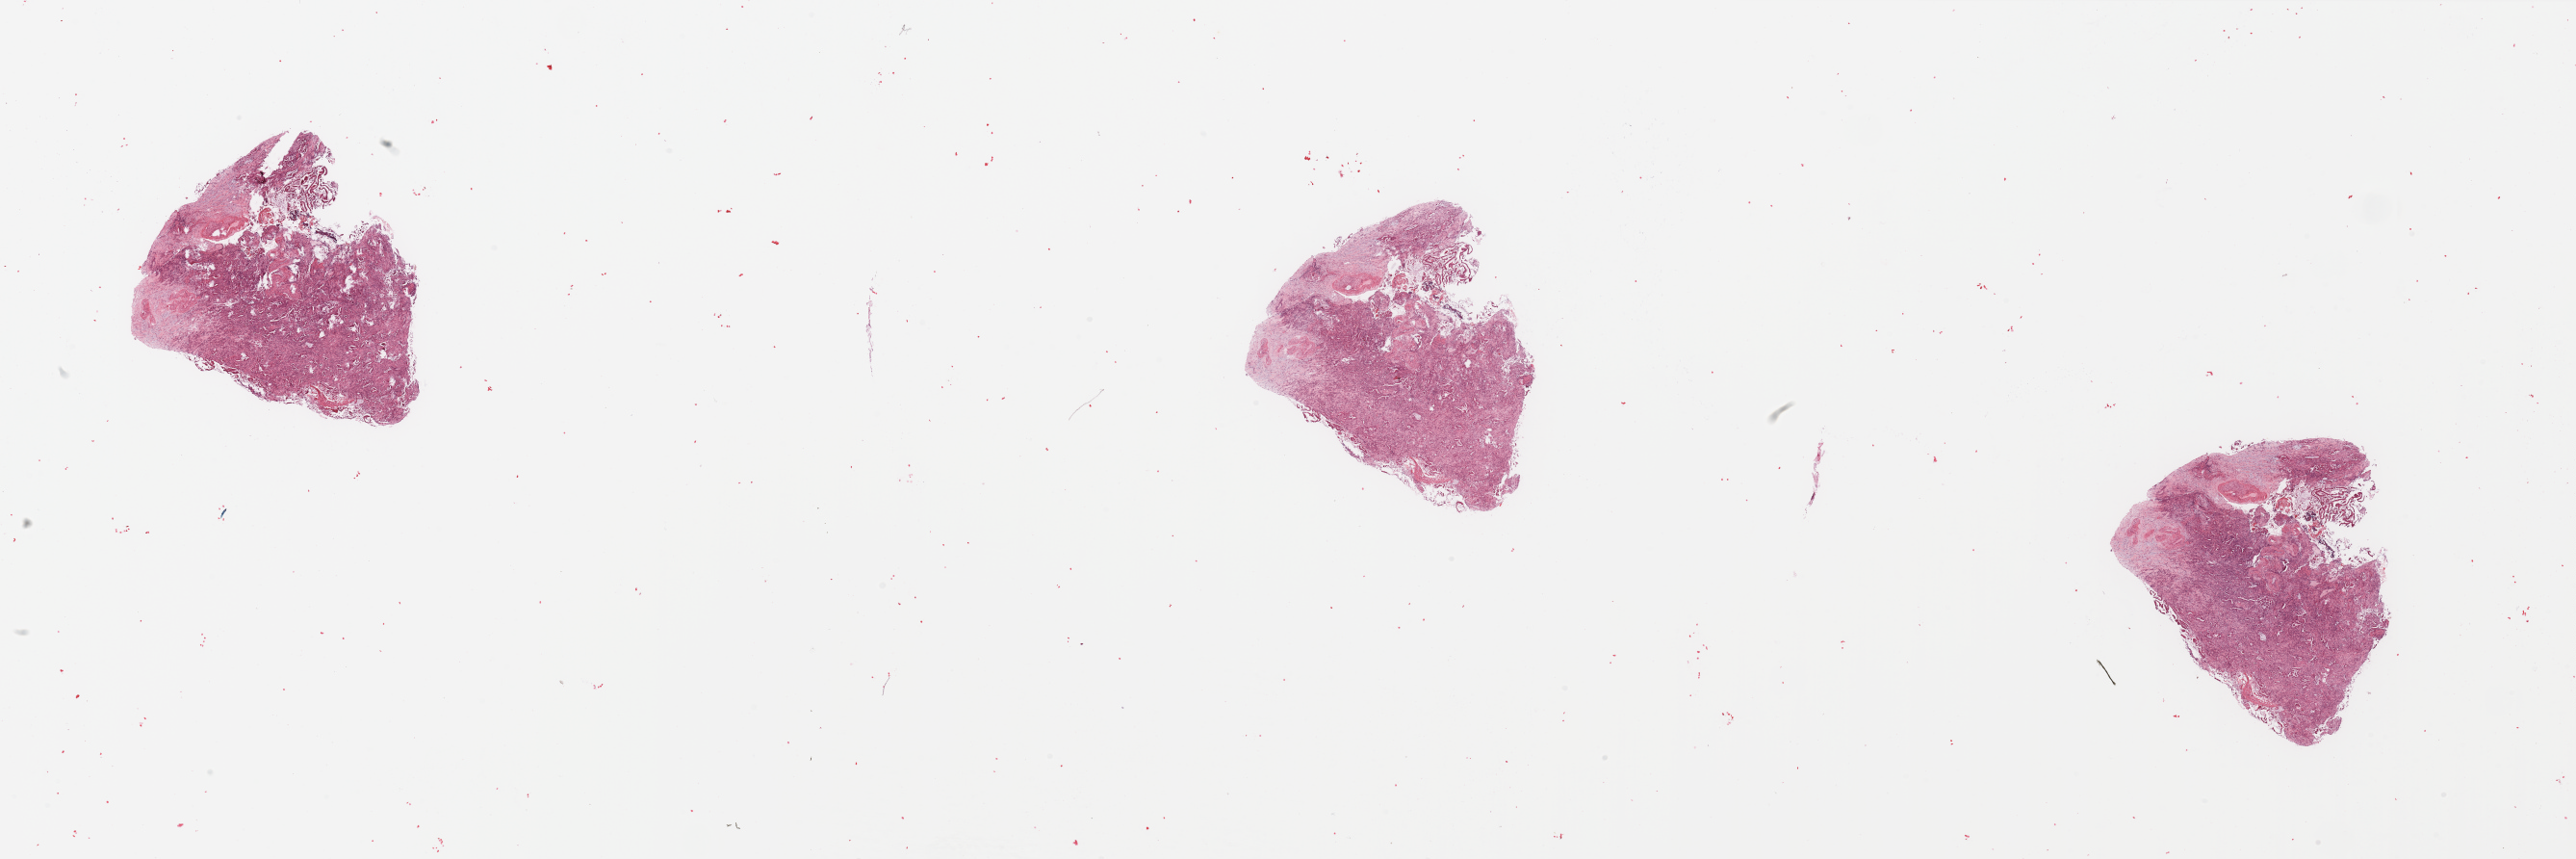
Hematoxylin and eosin (H&E) stained whole-slide image, low-resolution overview of the scanned area, about 42.3 x 14.1 mm (acquisition: 20x scan); tumour tissue sample, sampled site: pancreas. Female, 68 y/o. Histologic grade: G2 (moderately differentiated). Composition of this section per pathologist review: tumour nuclei 30%, necrosis 2%.
AJCC pathologic stage: IB. Diagnosis: Infiltrating duct carcinoma, NOS. Primary tumour site (as recorded): head.